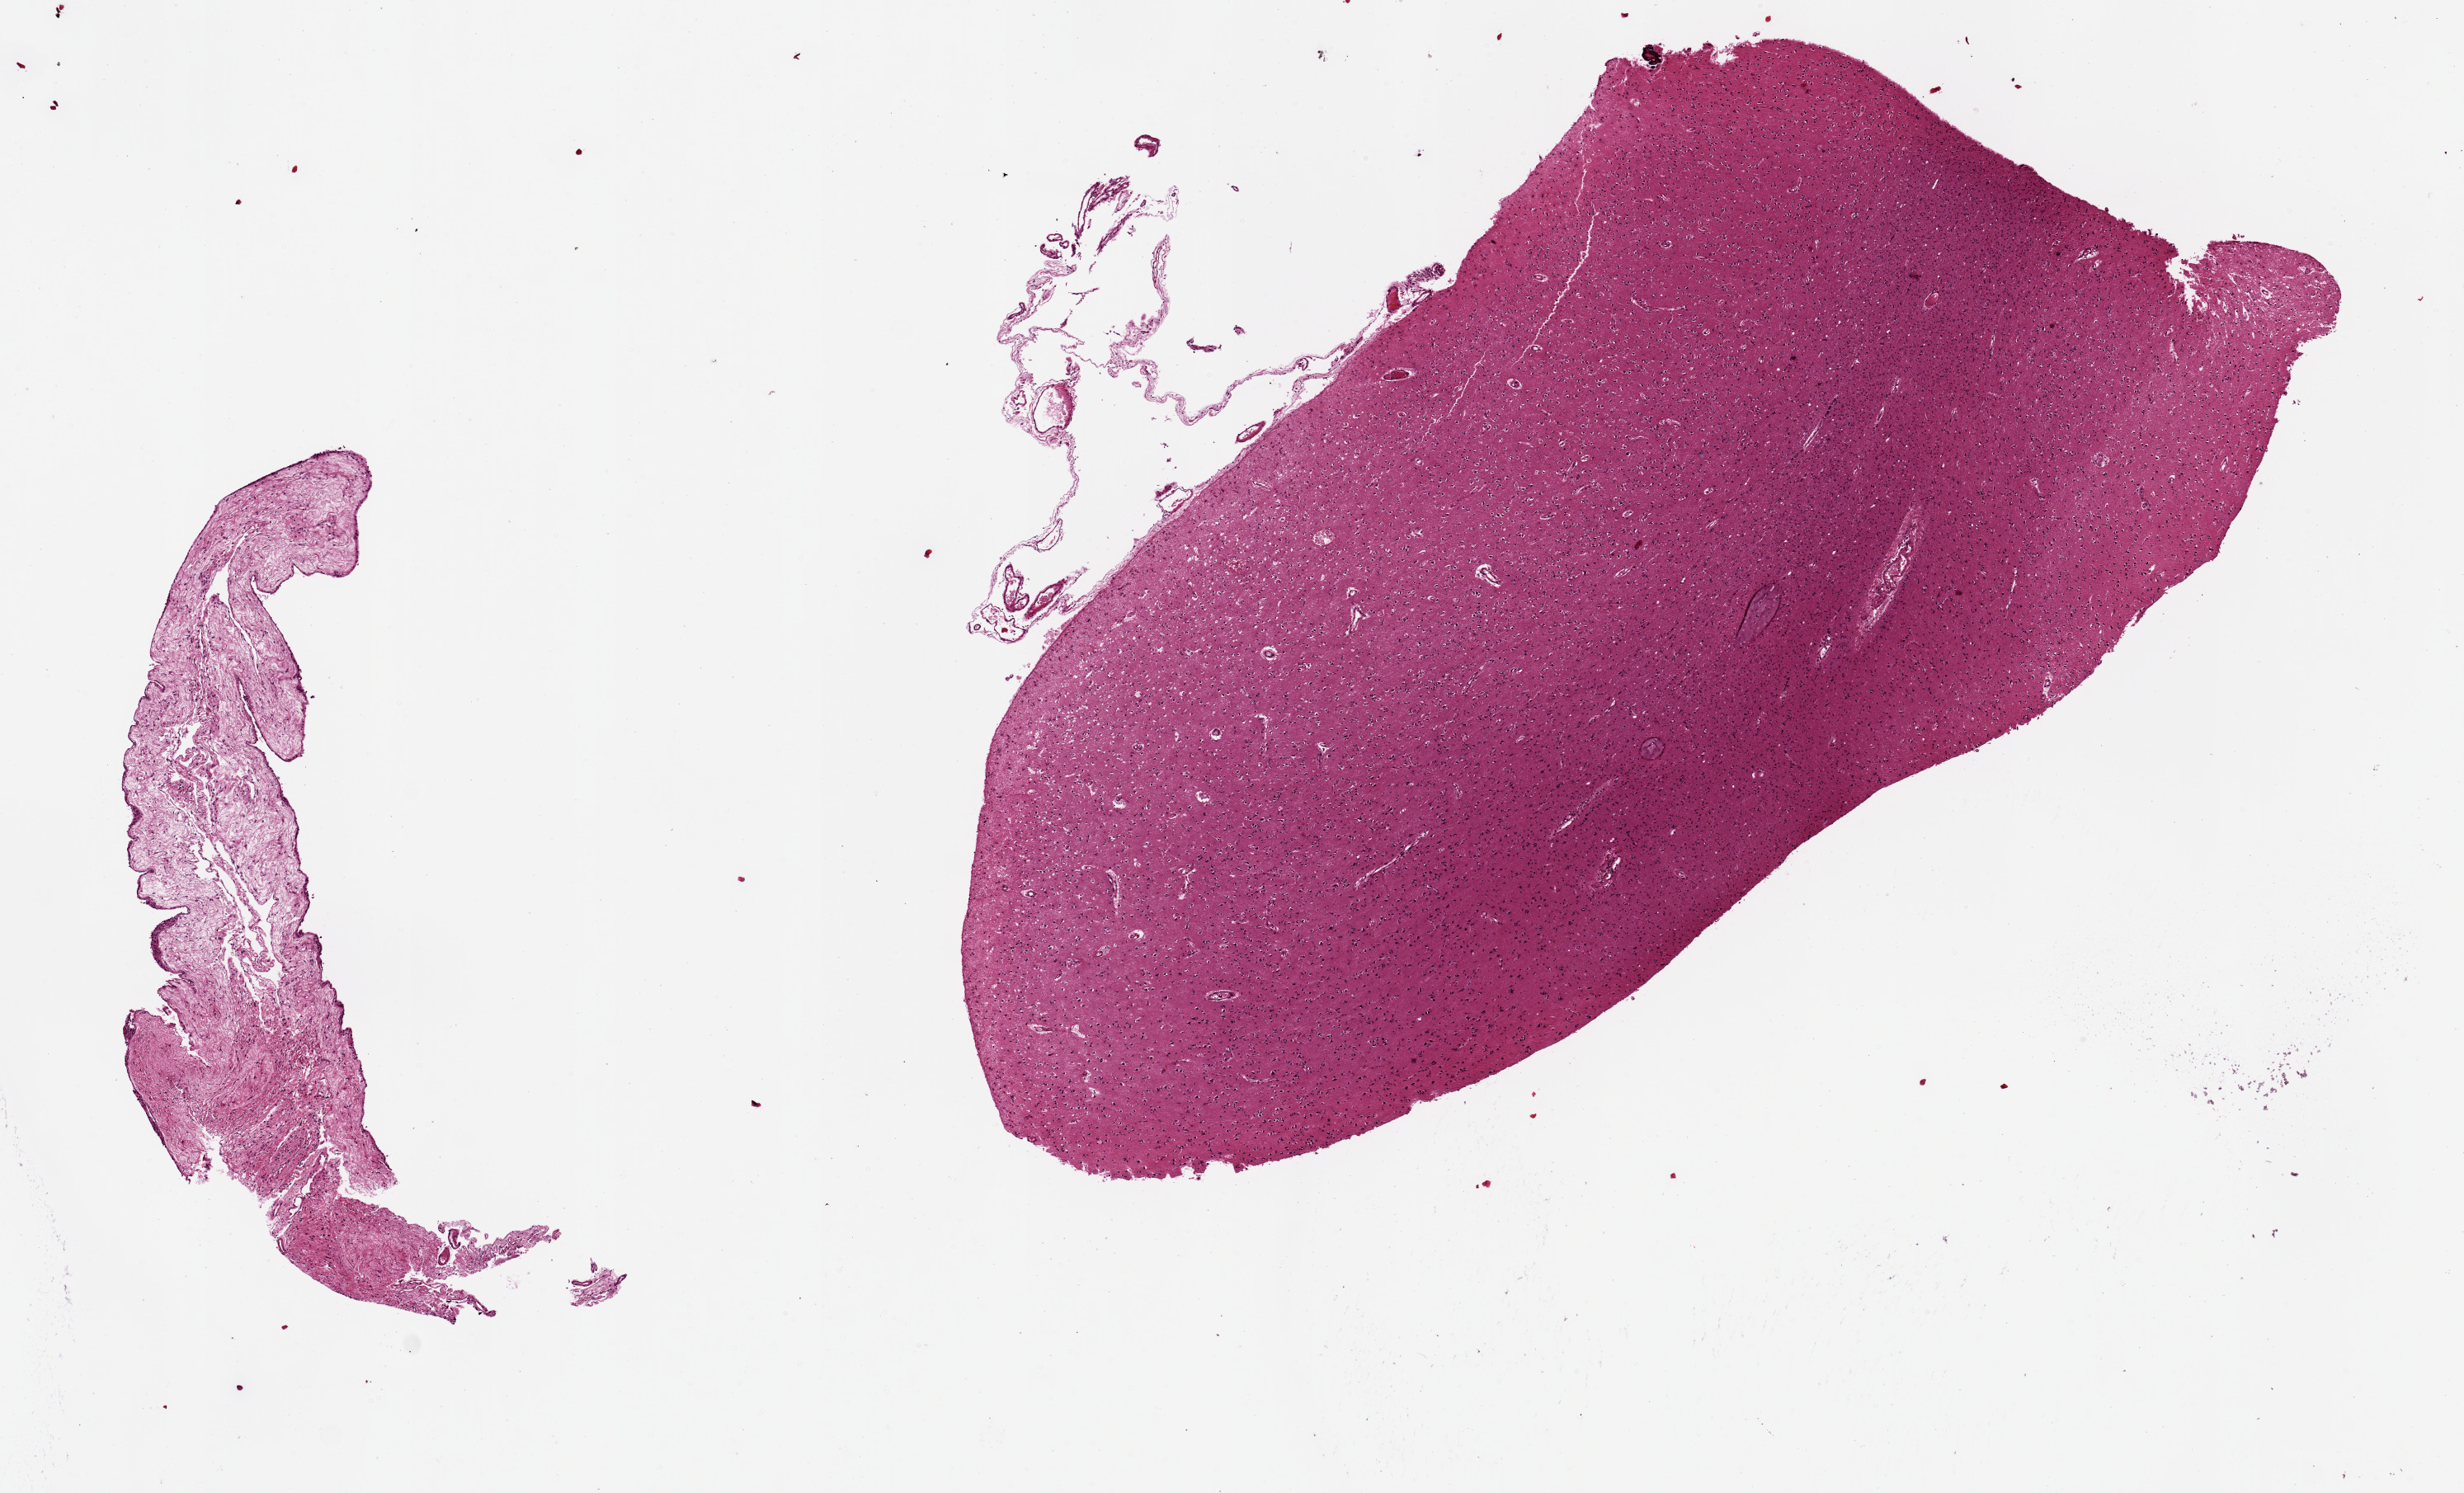
Digitized H&E-stained section, a low-resolution overview of the entire scanned area, about 11.8 x 7.2 mm; PAXgene-fixed, paraffin-embedded tissue; sampled site (target tissue): cerebral cortex; tissue donor sample. Donor sex: female.
Review note (as recorded): Fragment of meninges present in block.